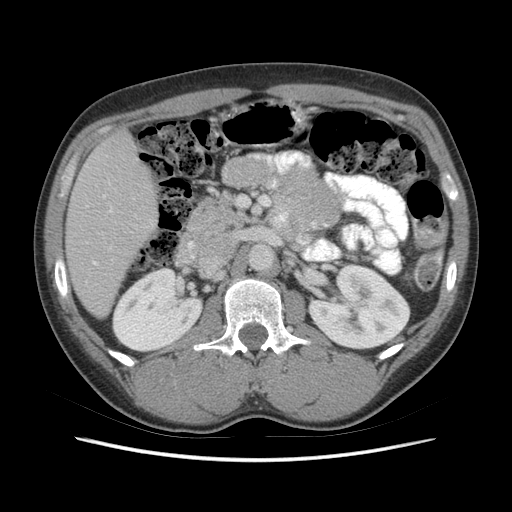
Contrast-enhanced abdominal CT (liver protocol), one axial slice; slice 23 of 73 in the series (ordered by position); reconstruction kernel STANDARD; 140 kVp; soft-tissue window (W 400 / L 40 HU); 2.5 mm slice thickness; 512 × 512 image matrix, field of view 360 × 360 mm. Case-level facts recorded for this patient, not image findings: diagnosis: hepatocellular carcinoma (patient treated with transarterial chemoembolisation; whether this scan precedes or follows treatment is not stated here); TNM stage (as recorded): Stage-IIIA; Child-Pugh class: A.
Structures marked on this image (semi-automatically segmented with operator editing):
- liver parenchyma outside the tumour (the mass and vessels are separate outlines, so this box may not span the whole liver): bounding box <66,132,158,316> (left, top, right, bottom; pixels)
- liver vessels: <92,195,111,265>